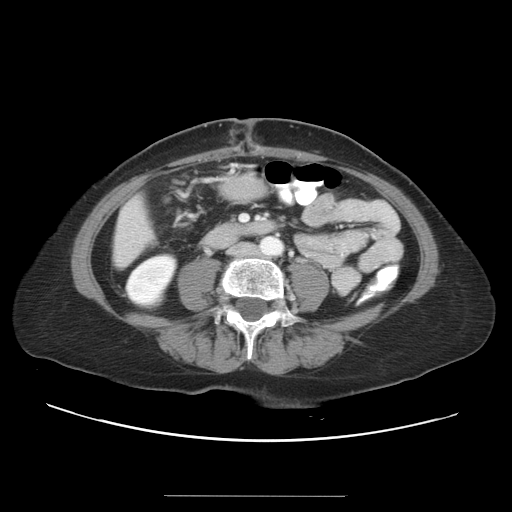
Contrast-enhanced abdominal CT, one axial slice. Position 3 of 34 along the scan axis. Intravenous contrast given. Soft-tissue window (W 400 / L 40 HU). 5 mm slice thickness. 512 × 512 image matrix. Female patient, age 69 years. Case-level facts recorded for this patient, not image findings: diagnosis: colorectal cancer liver metastases, imaged before liver resection; multiple liver metastases: yes; largest metastasis: 1.4 cm; disease in both lobes: yes.
Annotated regions visible in this slice (outlined manually by an expert reader):
- liver: bounding box <115,197,154,266> (left, top, right, bottom; pixels)
- planned liver remnant (the part of the liver to remain after resection): <115,221,154,266>
- portal vein (with intrahepatic branches): <241,215,248,221>